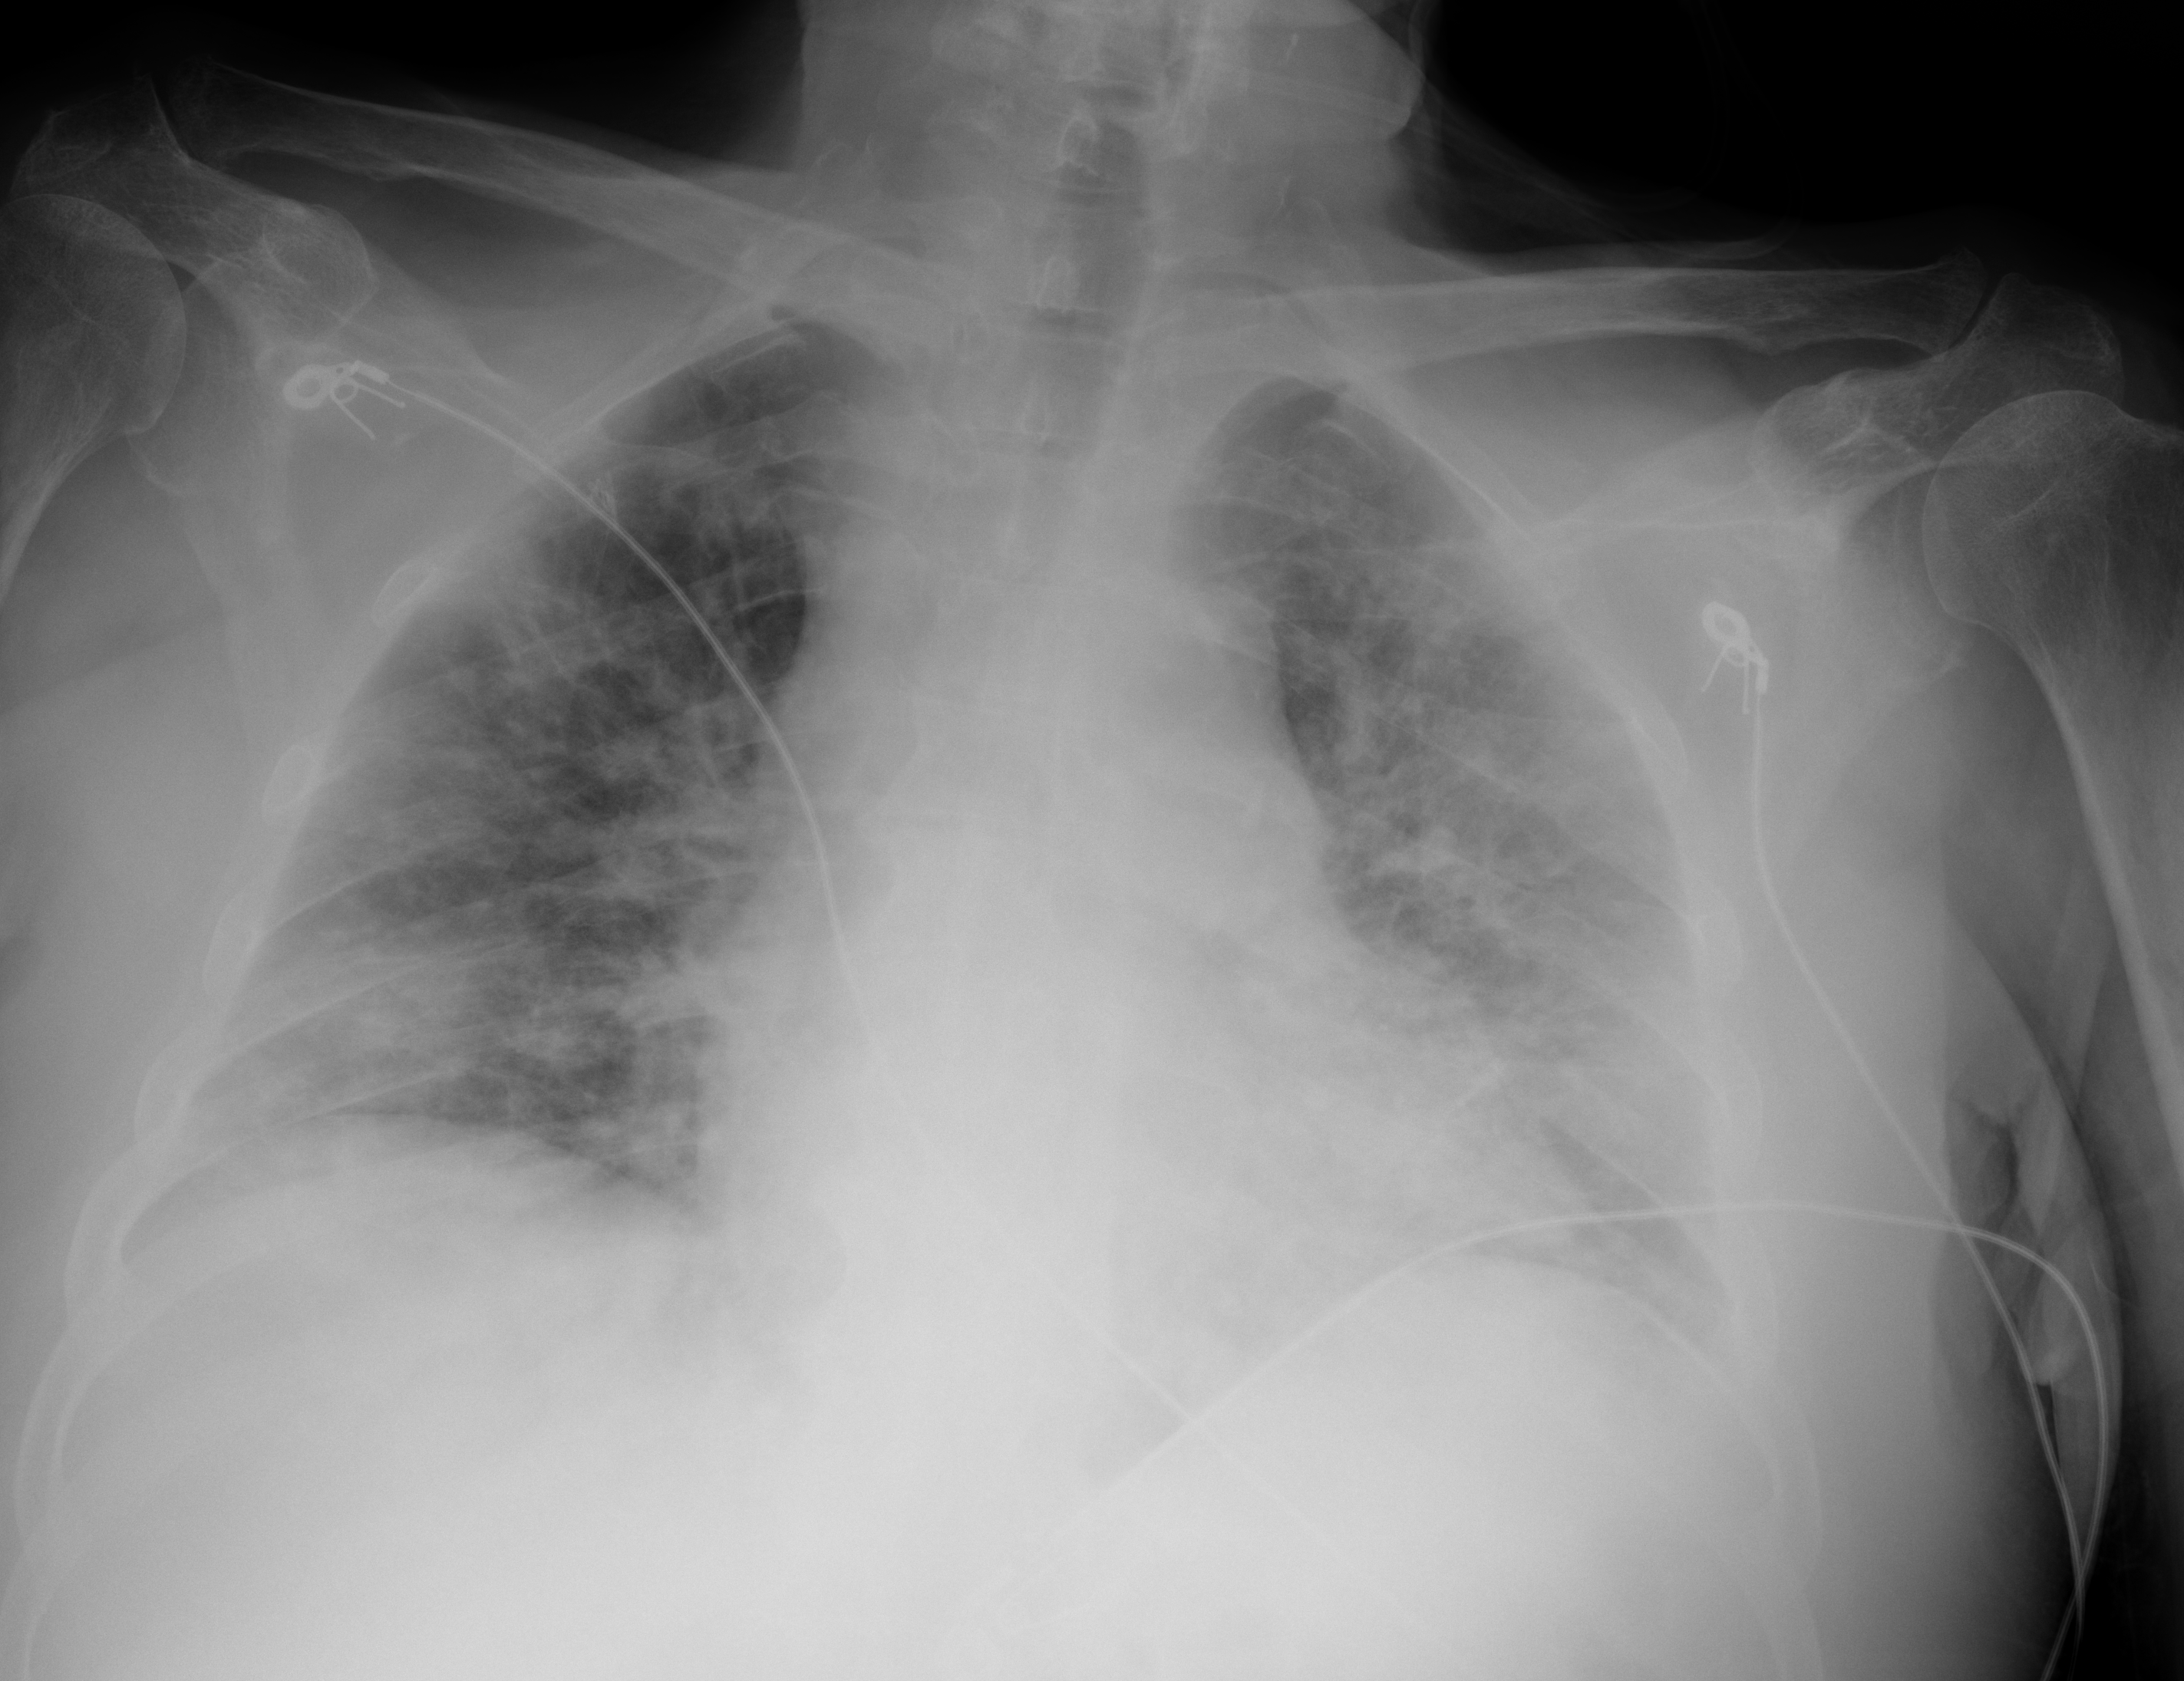
Portable chest radiograph, AP projection. Male patient, age 71 years; COVID-19 (test-positive).
Radiologist key findings (as recorded): There are confluent bilateral airspace opacities with a mid and lower lung predominance, more prominent on the left than the right, which represent multifocal infection.